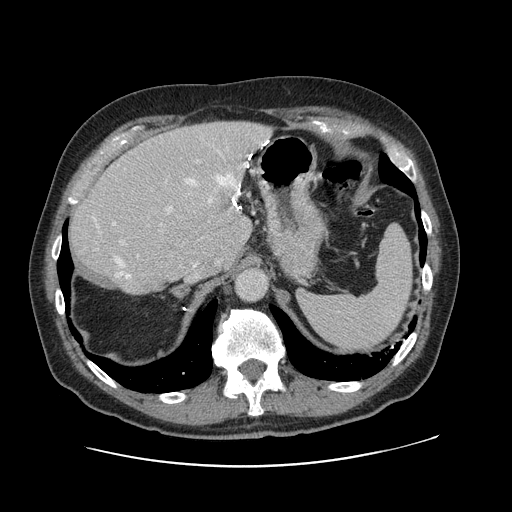
Contrast-enhanced abdominal CT, one axial slice; position 84 of 138 along the scan axis; 120 kVp; intravenous contrast given; soft-tissue window (W 400 / L 40 HU); 2.5 mm slice thickness; 512 × 512 image matrix, field of view 402 × 402 mm. Male patient, age 71 years. Case-level facts recorded for this patient, not image findings: diagnosis: colorectal cancer liver metastases, imaged before liver resection; multiple liver metastases: no; largest metastasis: 3.3 cm; disease in both lobes: no.
Outlined on this slice (outlined manually by an expert reader):
- hepatic veins: bounding box (x1, y1, x2, y2) in pixels: (115, 140, 267, 279)
- liver: (69, 122, 270, 294)
- planned liver remnant (the part of the liver to remain after resection): (69, 151, 239, 294)
- portal vein (with intrahepatic branches): (119, 160, 200, 245)
- liver metastasis: (213, 189, 236, 211)